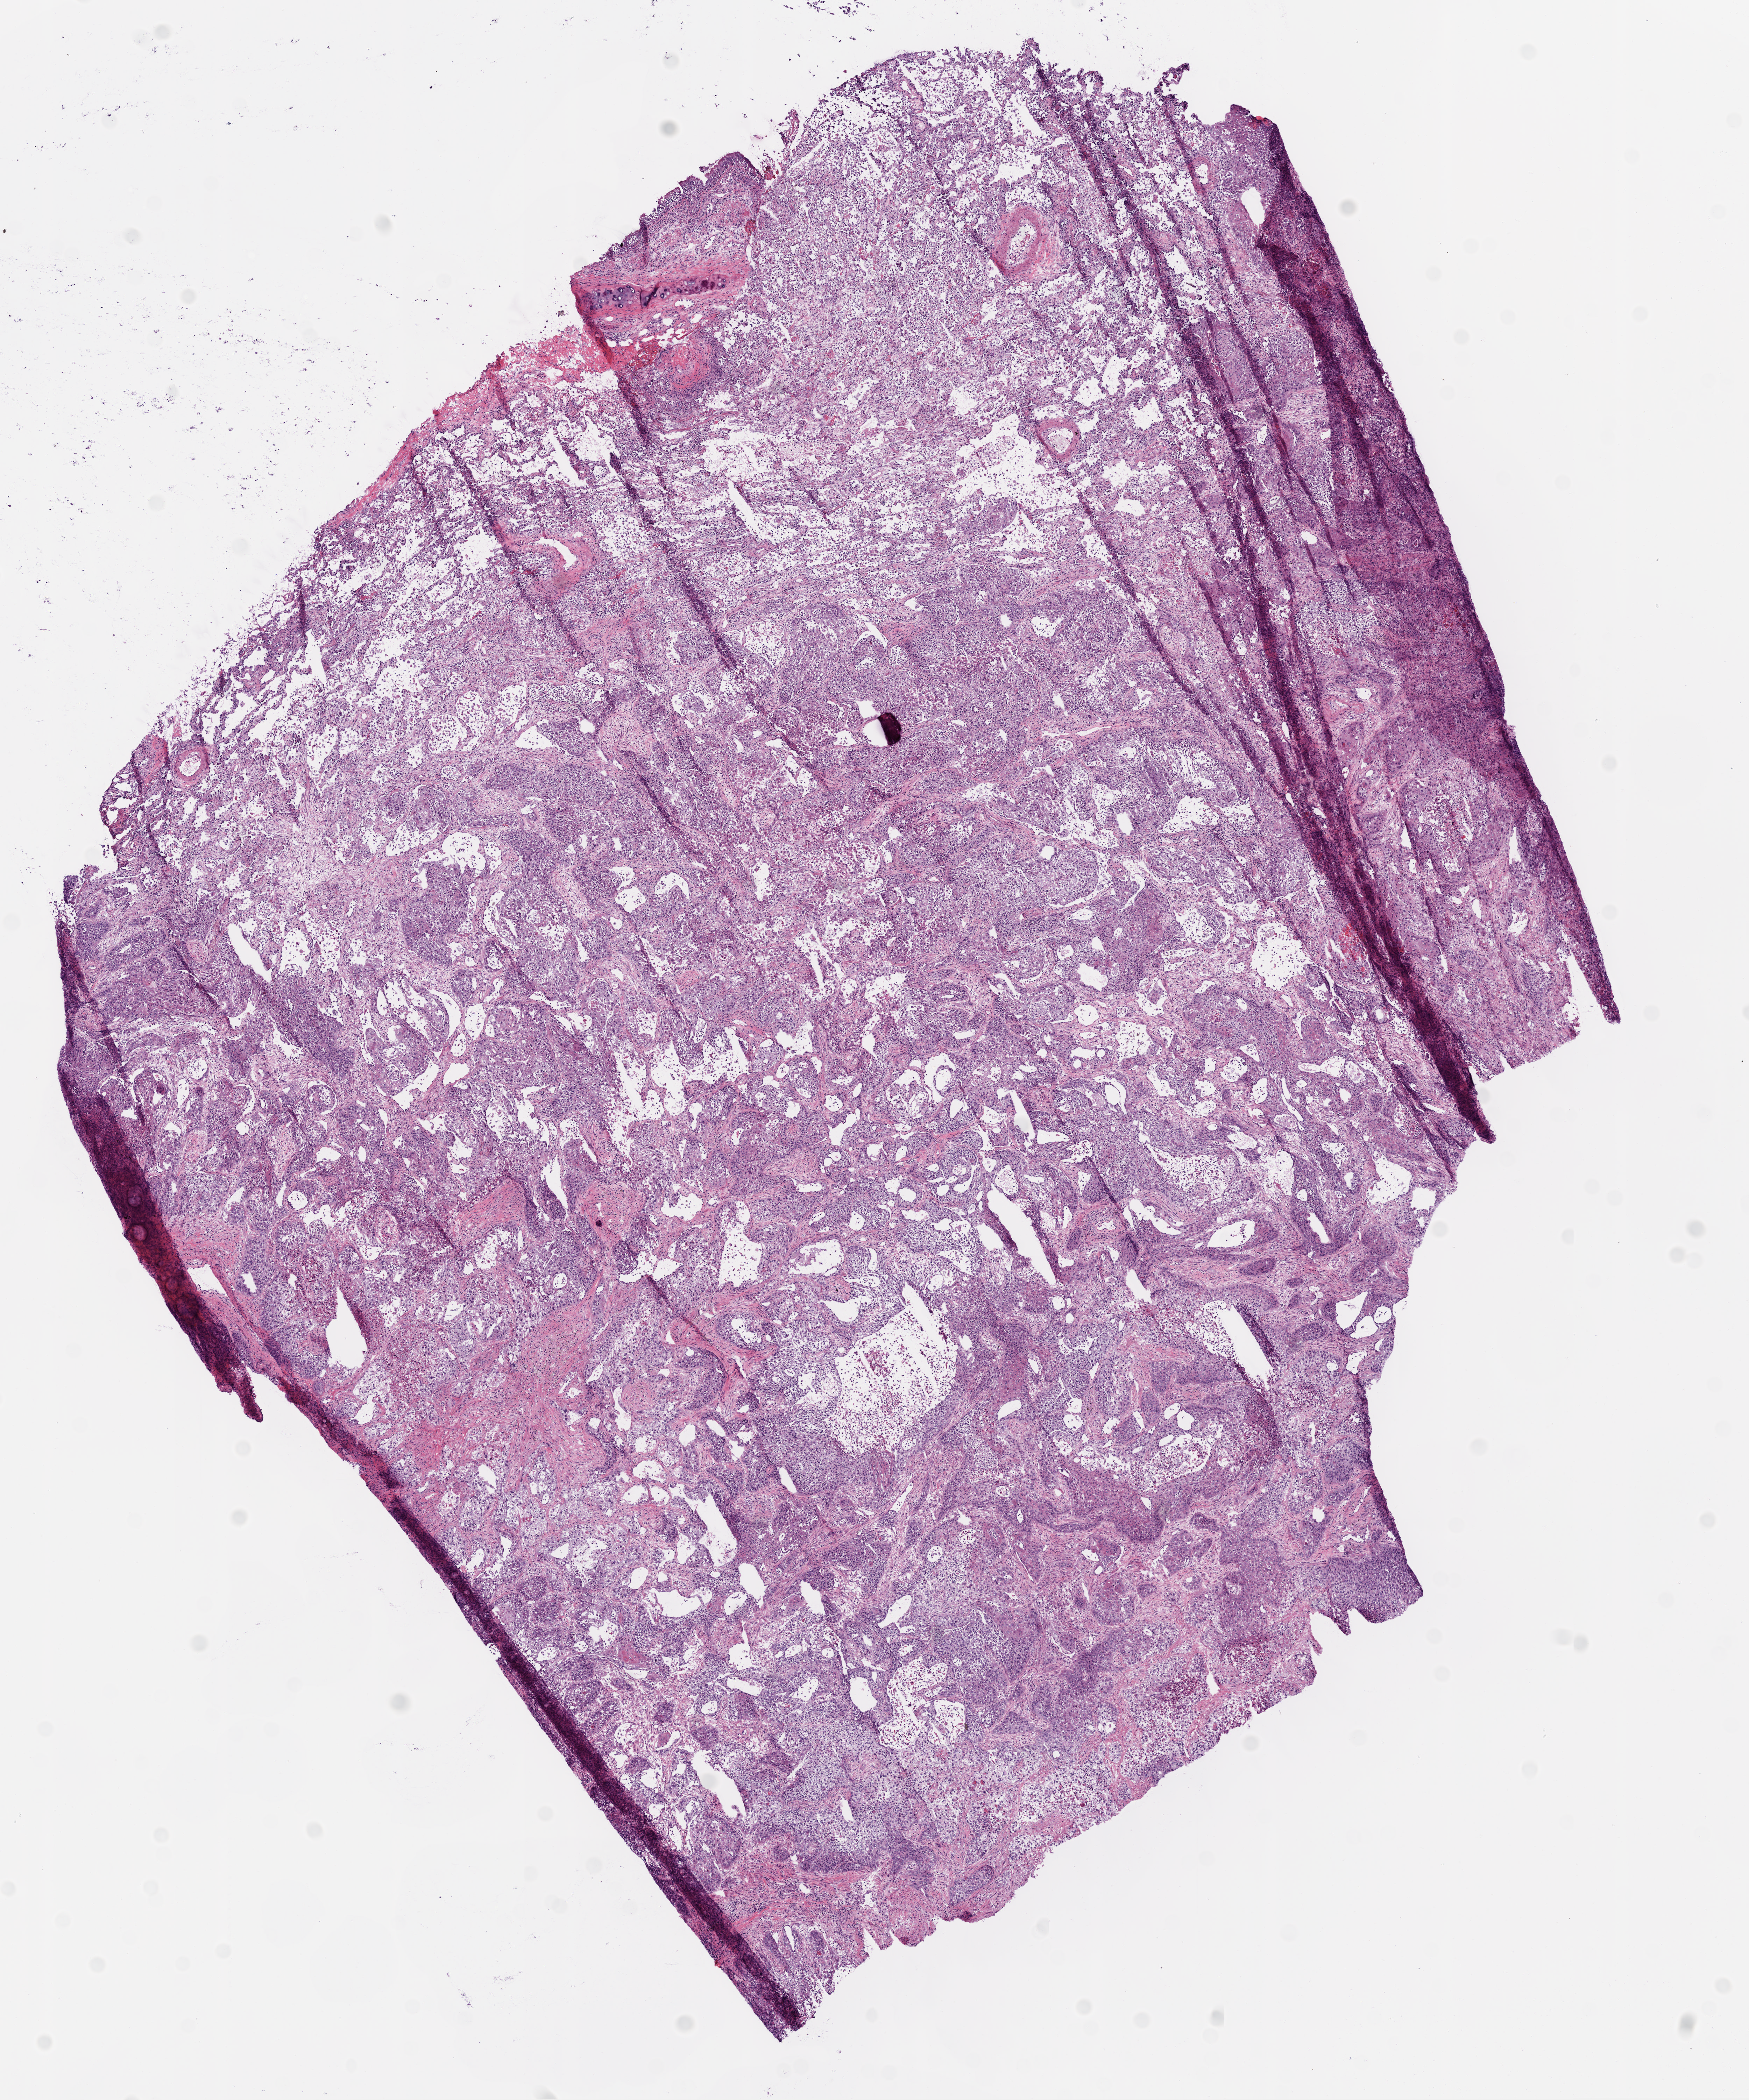
Whole-slide histology image, H&E-stained — a low-resolution overview of the entire scanned area, about 10.0 x 12.0 mm (slide scanned at 20x), frozen section, lung, primary tumour sample. Male, age 70 years at initial diagnosis. Slide review estimates, as recorded: tumour cells 75%, tumour nuclei 70%, normal cells 0%, stromal cells 15%, necrosis 10%.
* diagnosis: Squamous cell carcinoma, NOS (upper lobe, lung)
* AJCC pathologic stage: IB